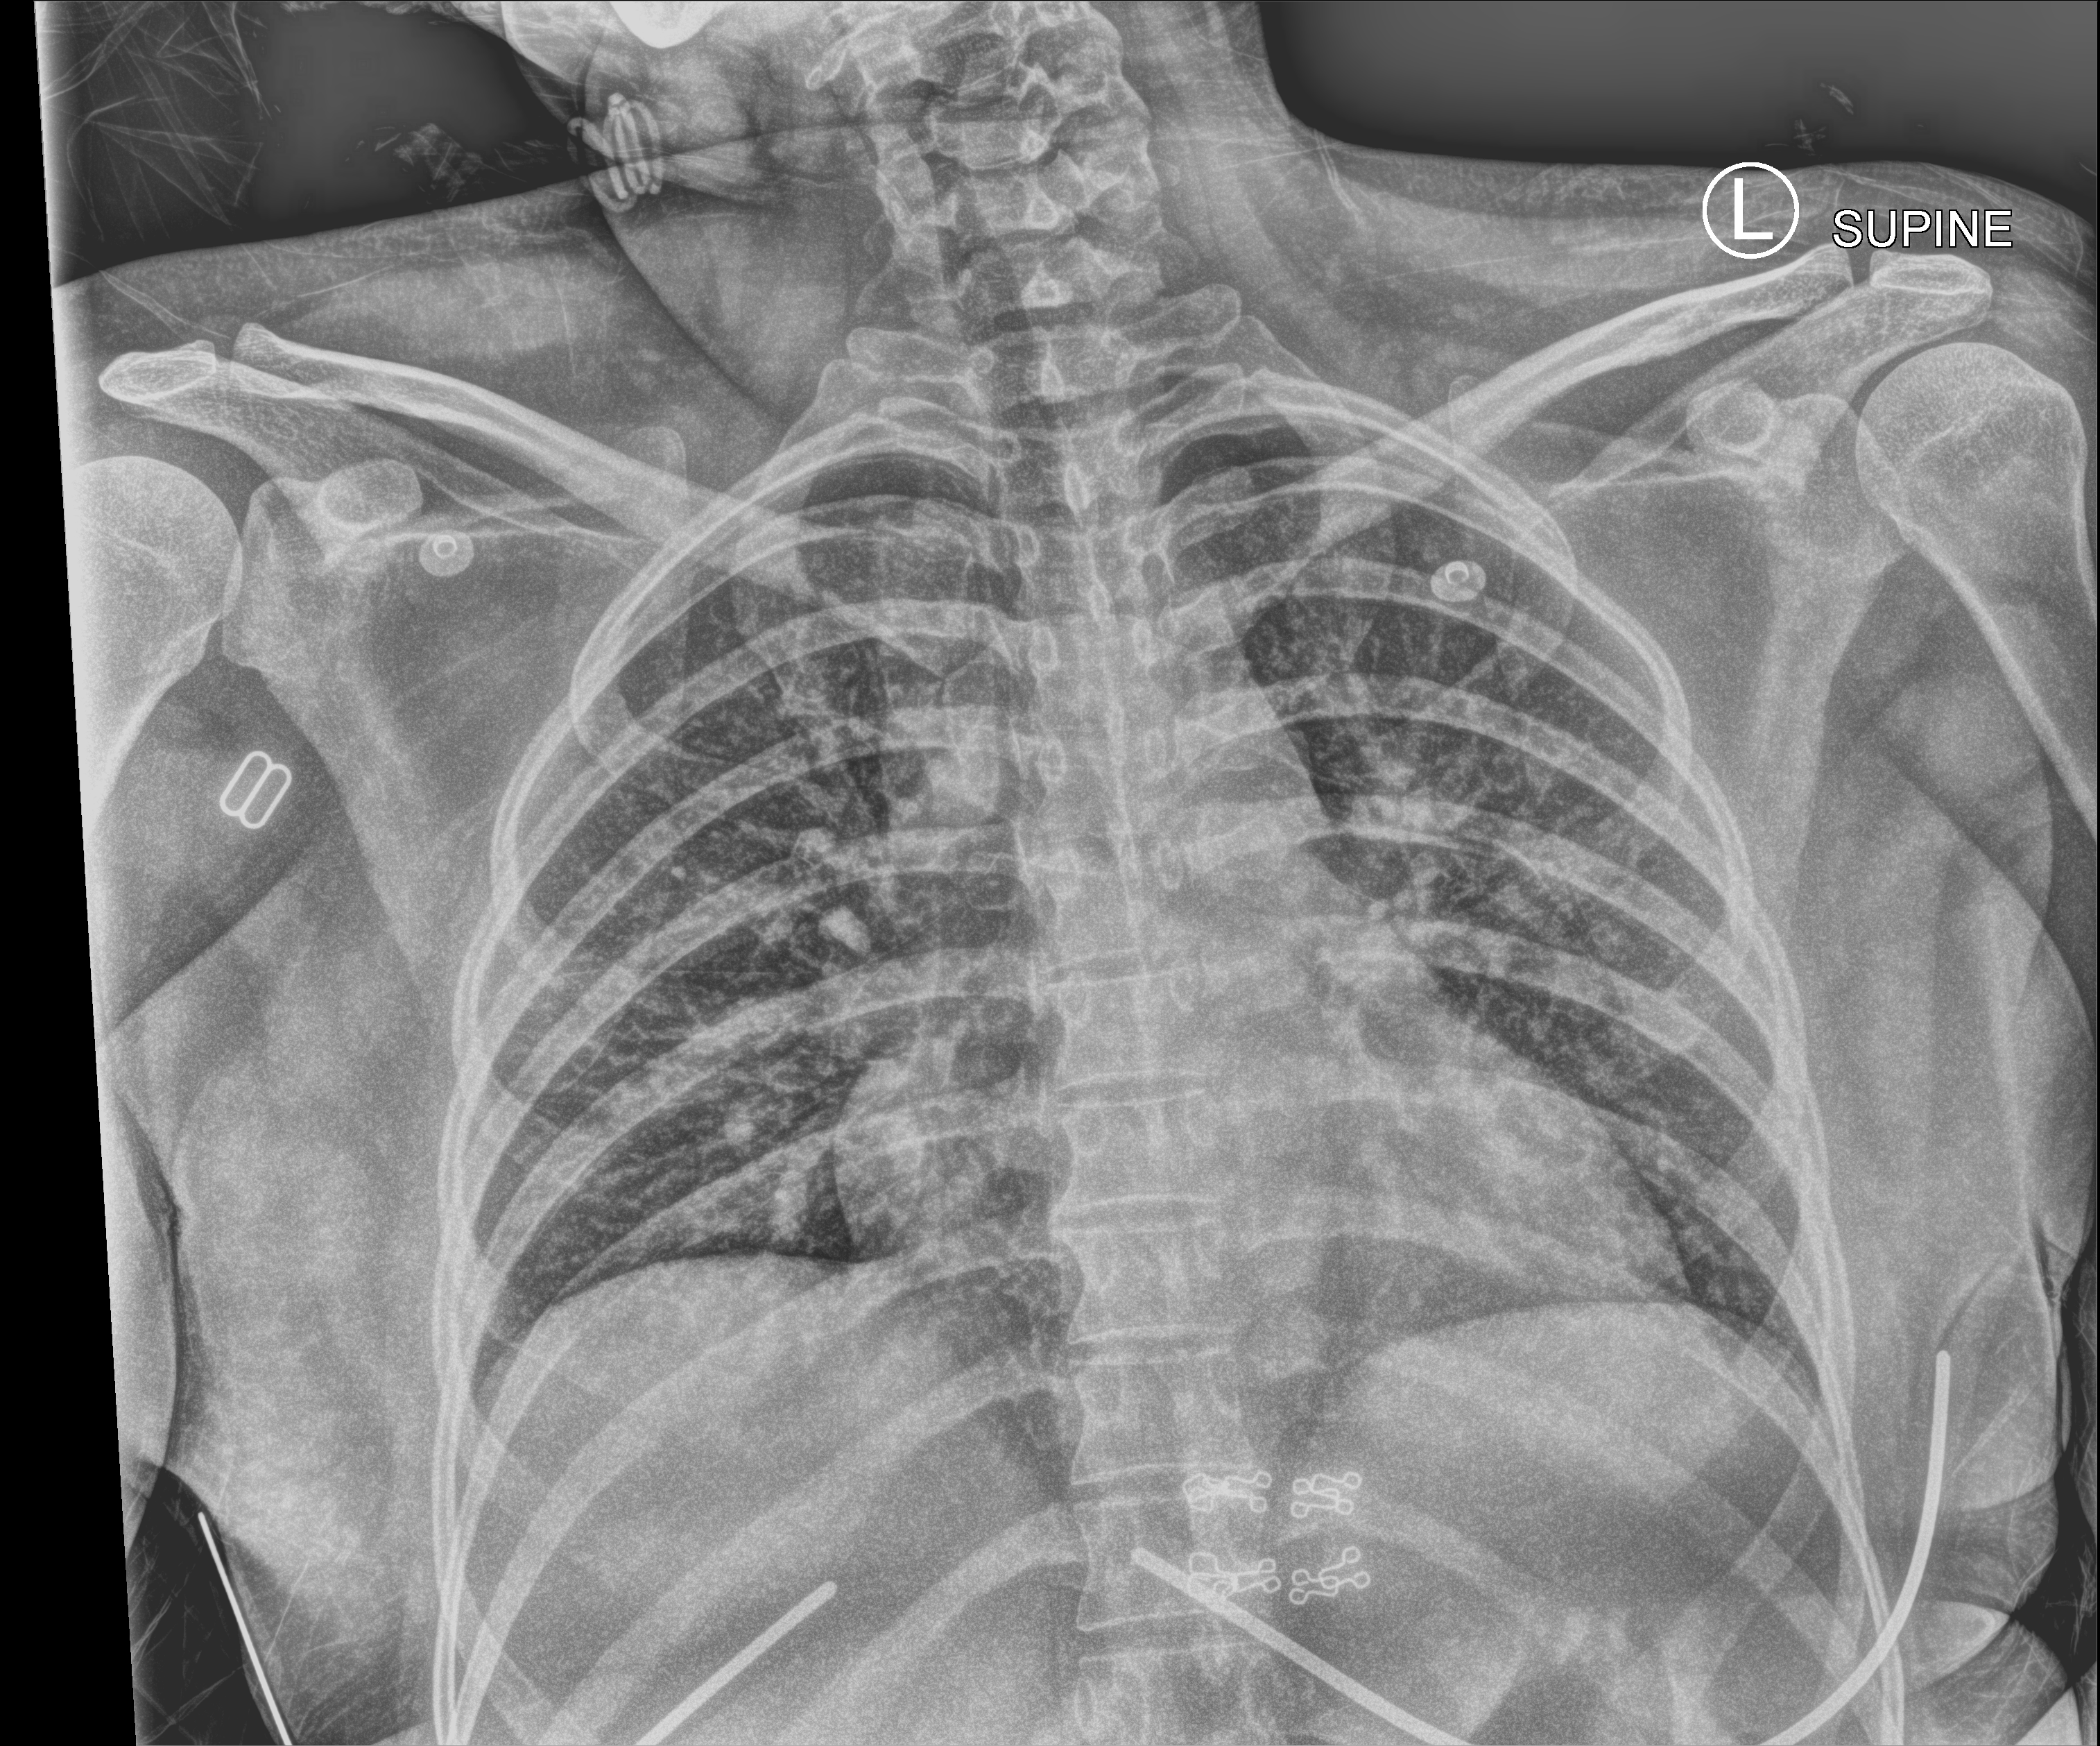
Bedside chest radiograph (computed radiography), anteroposterior (AP) projection. Patient hospitalised with COVID-19; female, aged 18–59 years.
From the hospital-stay record, not from the radiograph (when in the stay this image was taken is not recorded):
- diabetes (admission record): no